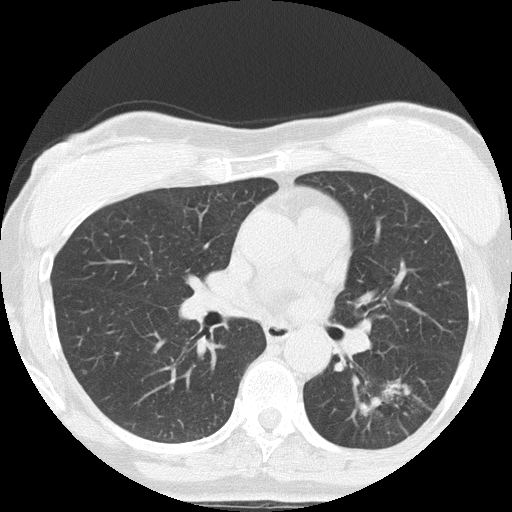
Axial slice from a low-dose chest CT screening exam. Third screening round (two years after baseline). Lung window (W 1500 / L -600 HU). 2 mm slice thickness. Slice 70 of 152 in the series. 512 × 512 image matrix. Female participant, aged 64 years at enrolment.
• Expert-annotated lung lesion, box from (x=366, y=365) to (x=456, y=441) px.
• The screening reader recorded 3 non-calcified nodules or masses ≥4 mm on this exam (right upper lobe, left lower lobe, right middle lobe); which of them this box marks is not recorded.
• Official screen result: positive, other.
• Later outcome: lung cancer diagnosed 212 days after this screen — adenocarcinoma, NOS, left lower lobe, moderately differentiated (G2), stage IA (AJCC 6th edition), 17 mm at pathology.